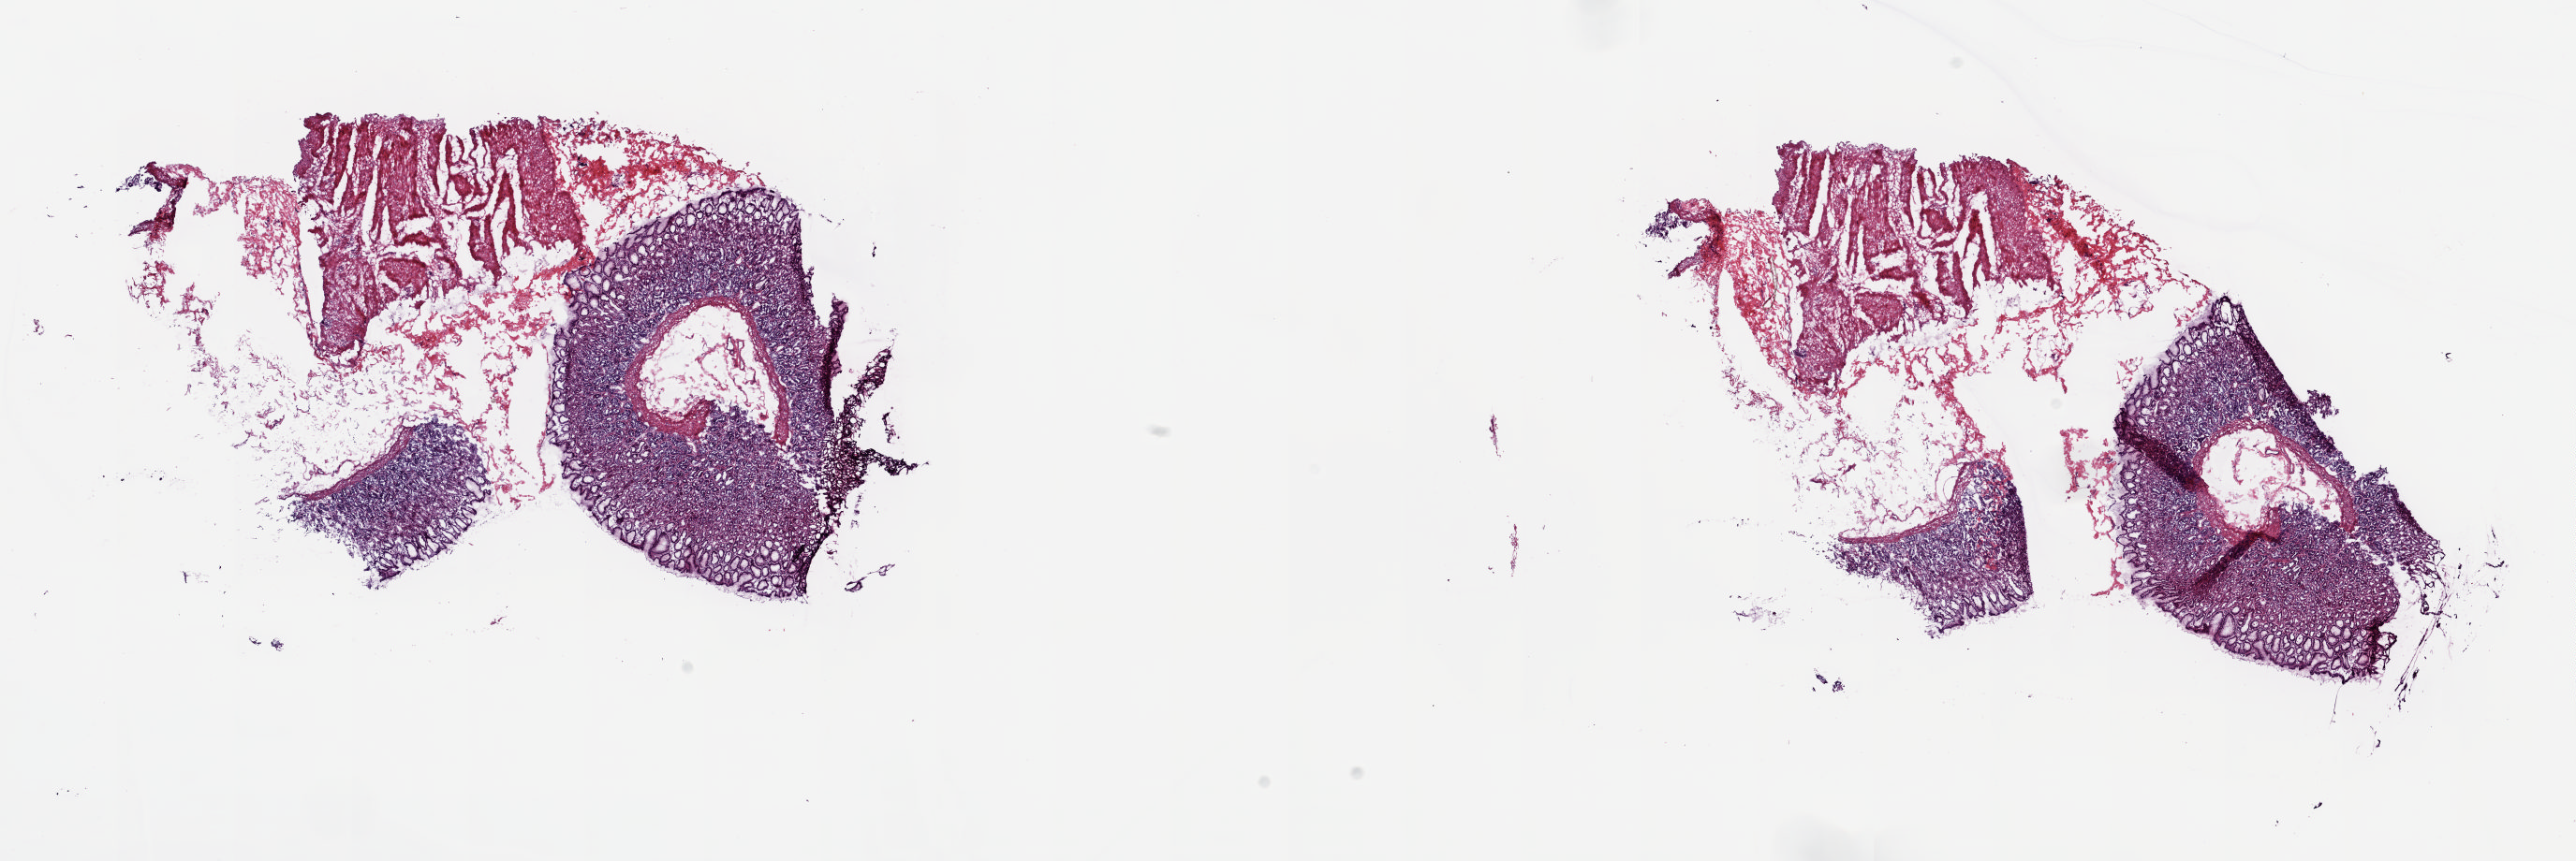
Hematoxylin and eosin (H&E) stained whole-slide image, low-resolution overview of the scanned area, about 21.8 x 7.3 mm (acquisition: 20x scan); frozen section; pancreas, solid tissue normal (non-tumour tissue) sample. Male patient; age at initial diagnosis 52 years. Pathologist review of this section (percent, as recorded): tumour cells 0%, tumour nuclei 0%, normal cells 60%, stromal cells 40%, necrosis 0%. Inflammatory infiltration, as recorded: lymphocyte infiltration 70%, monocyte infiltration 10%, neutrophil infiltration 10%.
• this section: solid tissue normal sample (biorepository sample class)
• patient diagnosis: Neuroendocrine carcinoma, NOS